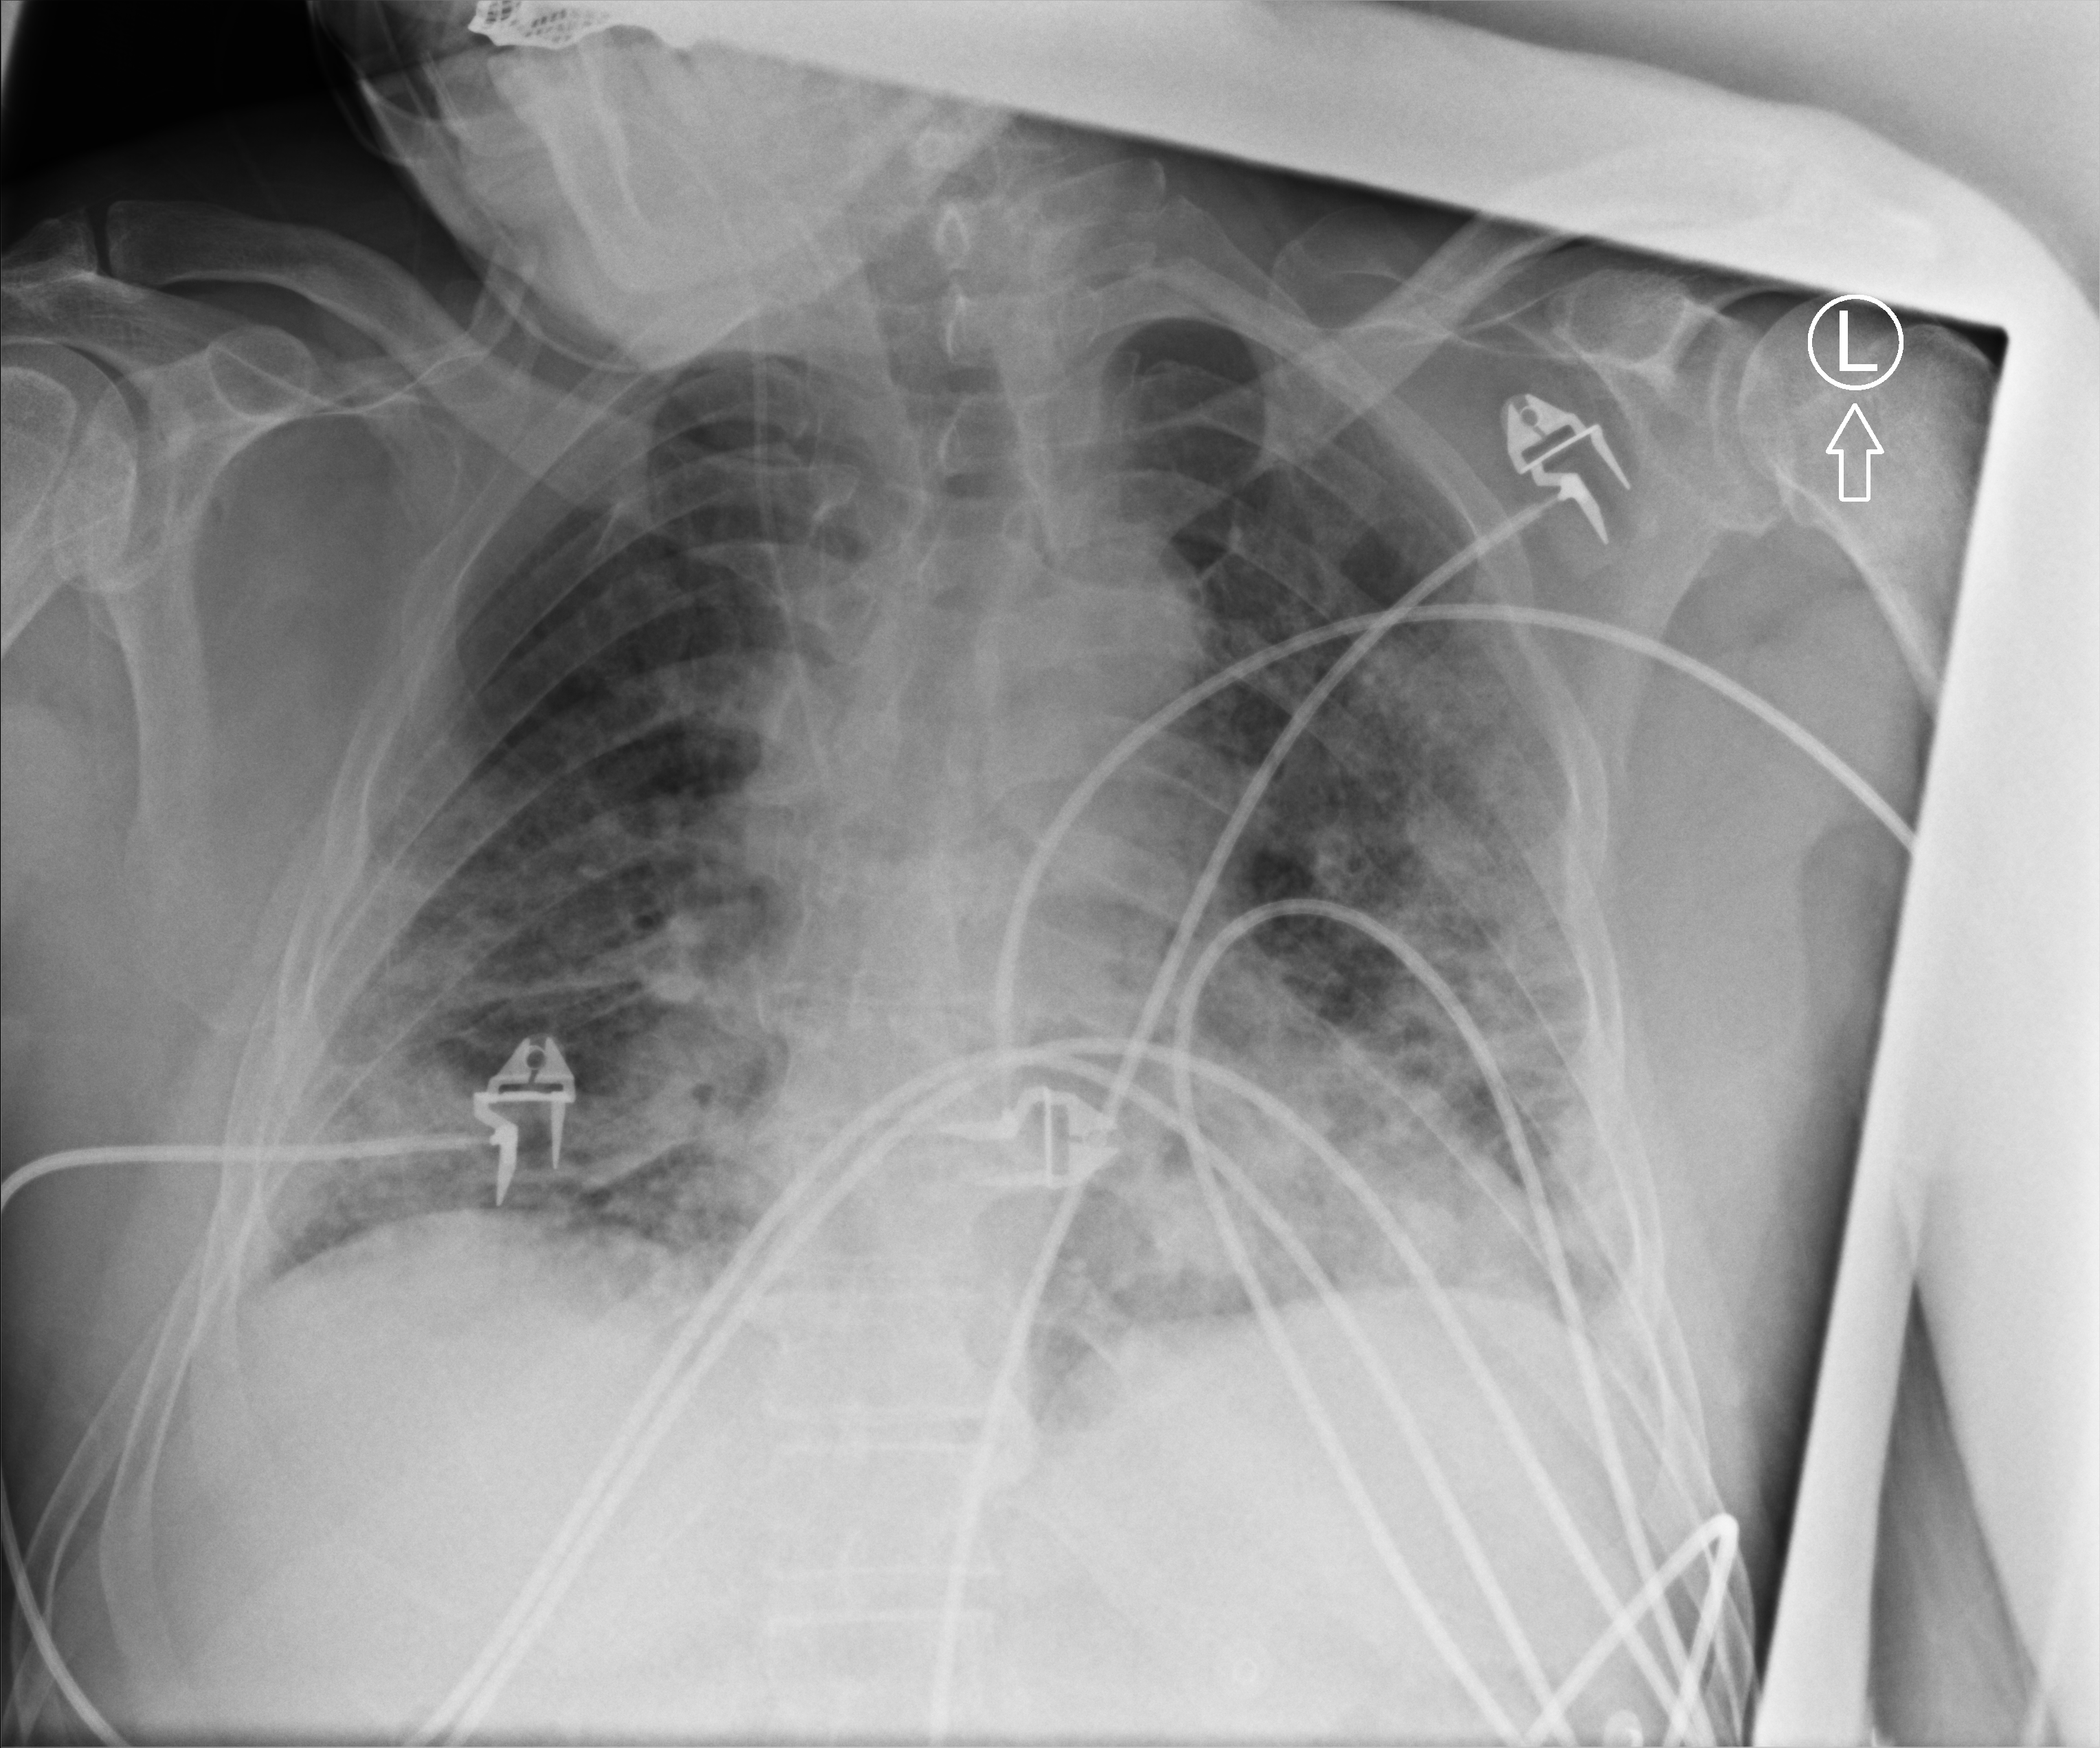
Bedside chest radiograph (computed radiography). Male patient hospitalised with COVID-19, age 60–74 years.
From the hospital-stay record, not from the radiograph (when in the stay this image was taken is not recorded):
- mechanically ventilated during this hospital stay: yes